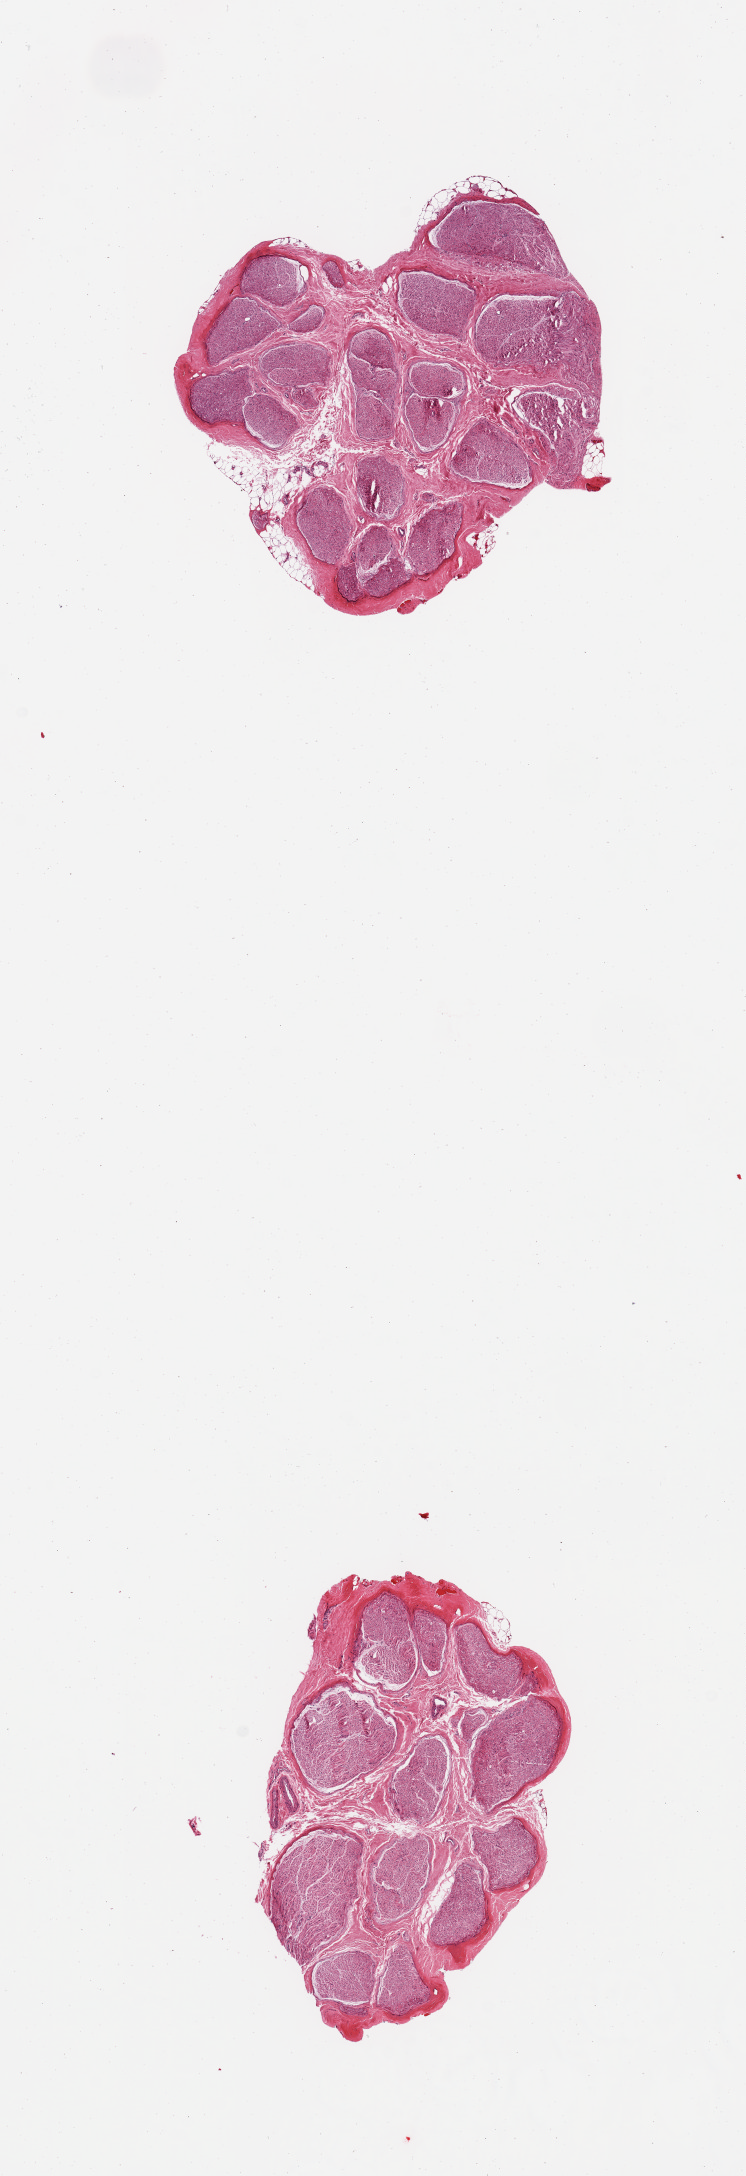
H&E whole-slide image, brightfield — whole scanned area (about 5.9 x 17.2 mm, acquisition: 20x scan) shown as a low-resolution overview, PAXgene-fixed, paraffin-embedded tissue, sampled site (target tissue): tibial nerve, donor tissue sample.
- pathologist's review note for this sample: 2 pieces, no significant adherent fat